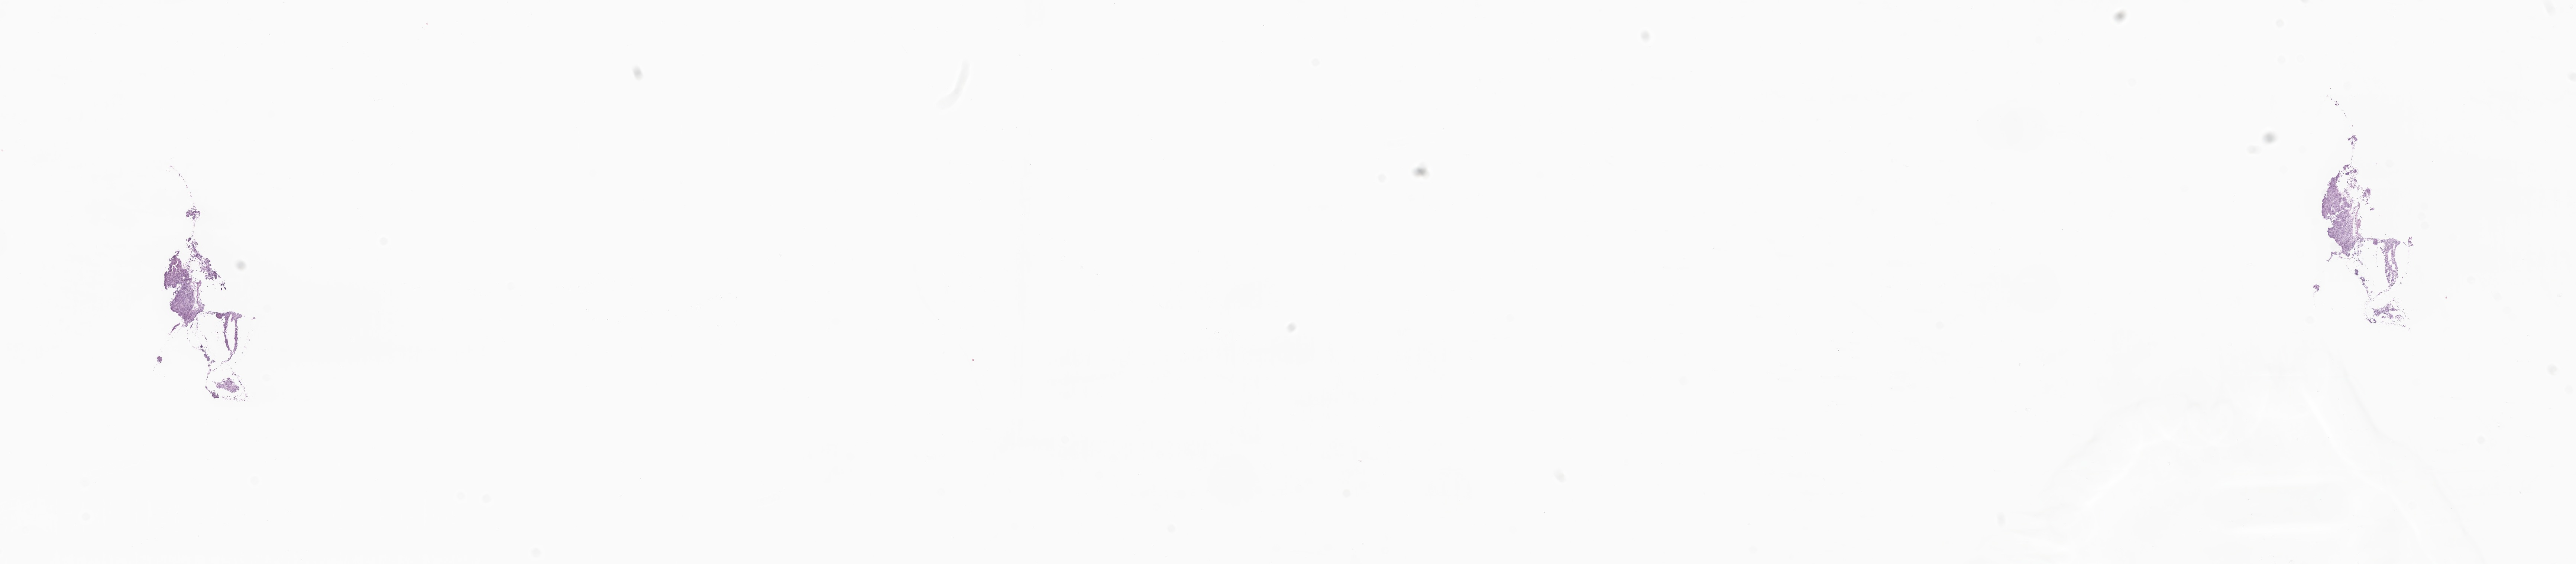
Whole-slide image, hematoxylin and eosin (H&E) stain of tumor tissue from the cerebral ventricle — whole scanned area (about 29.2 x 6.4 mm) shown as a low-resolution overview. Frozen section. Patient: female, age 71 months (5 years 11 months).
• diagnosis: Atypical teratoid/rhabdoid tumor